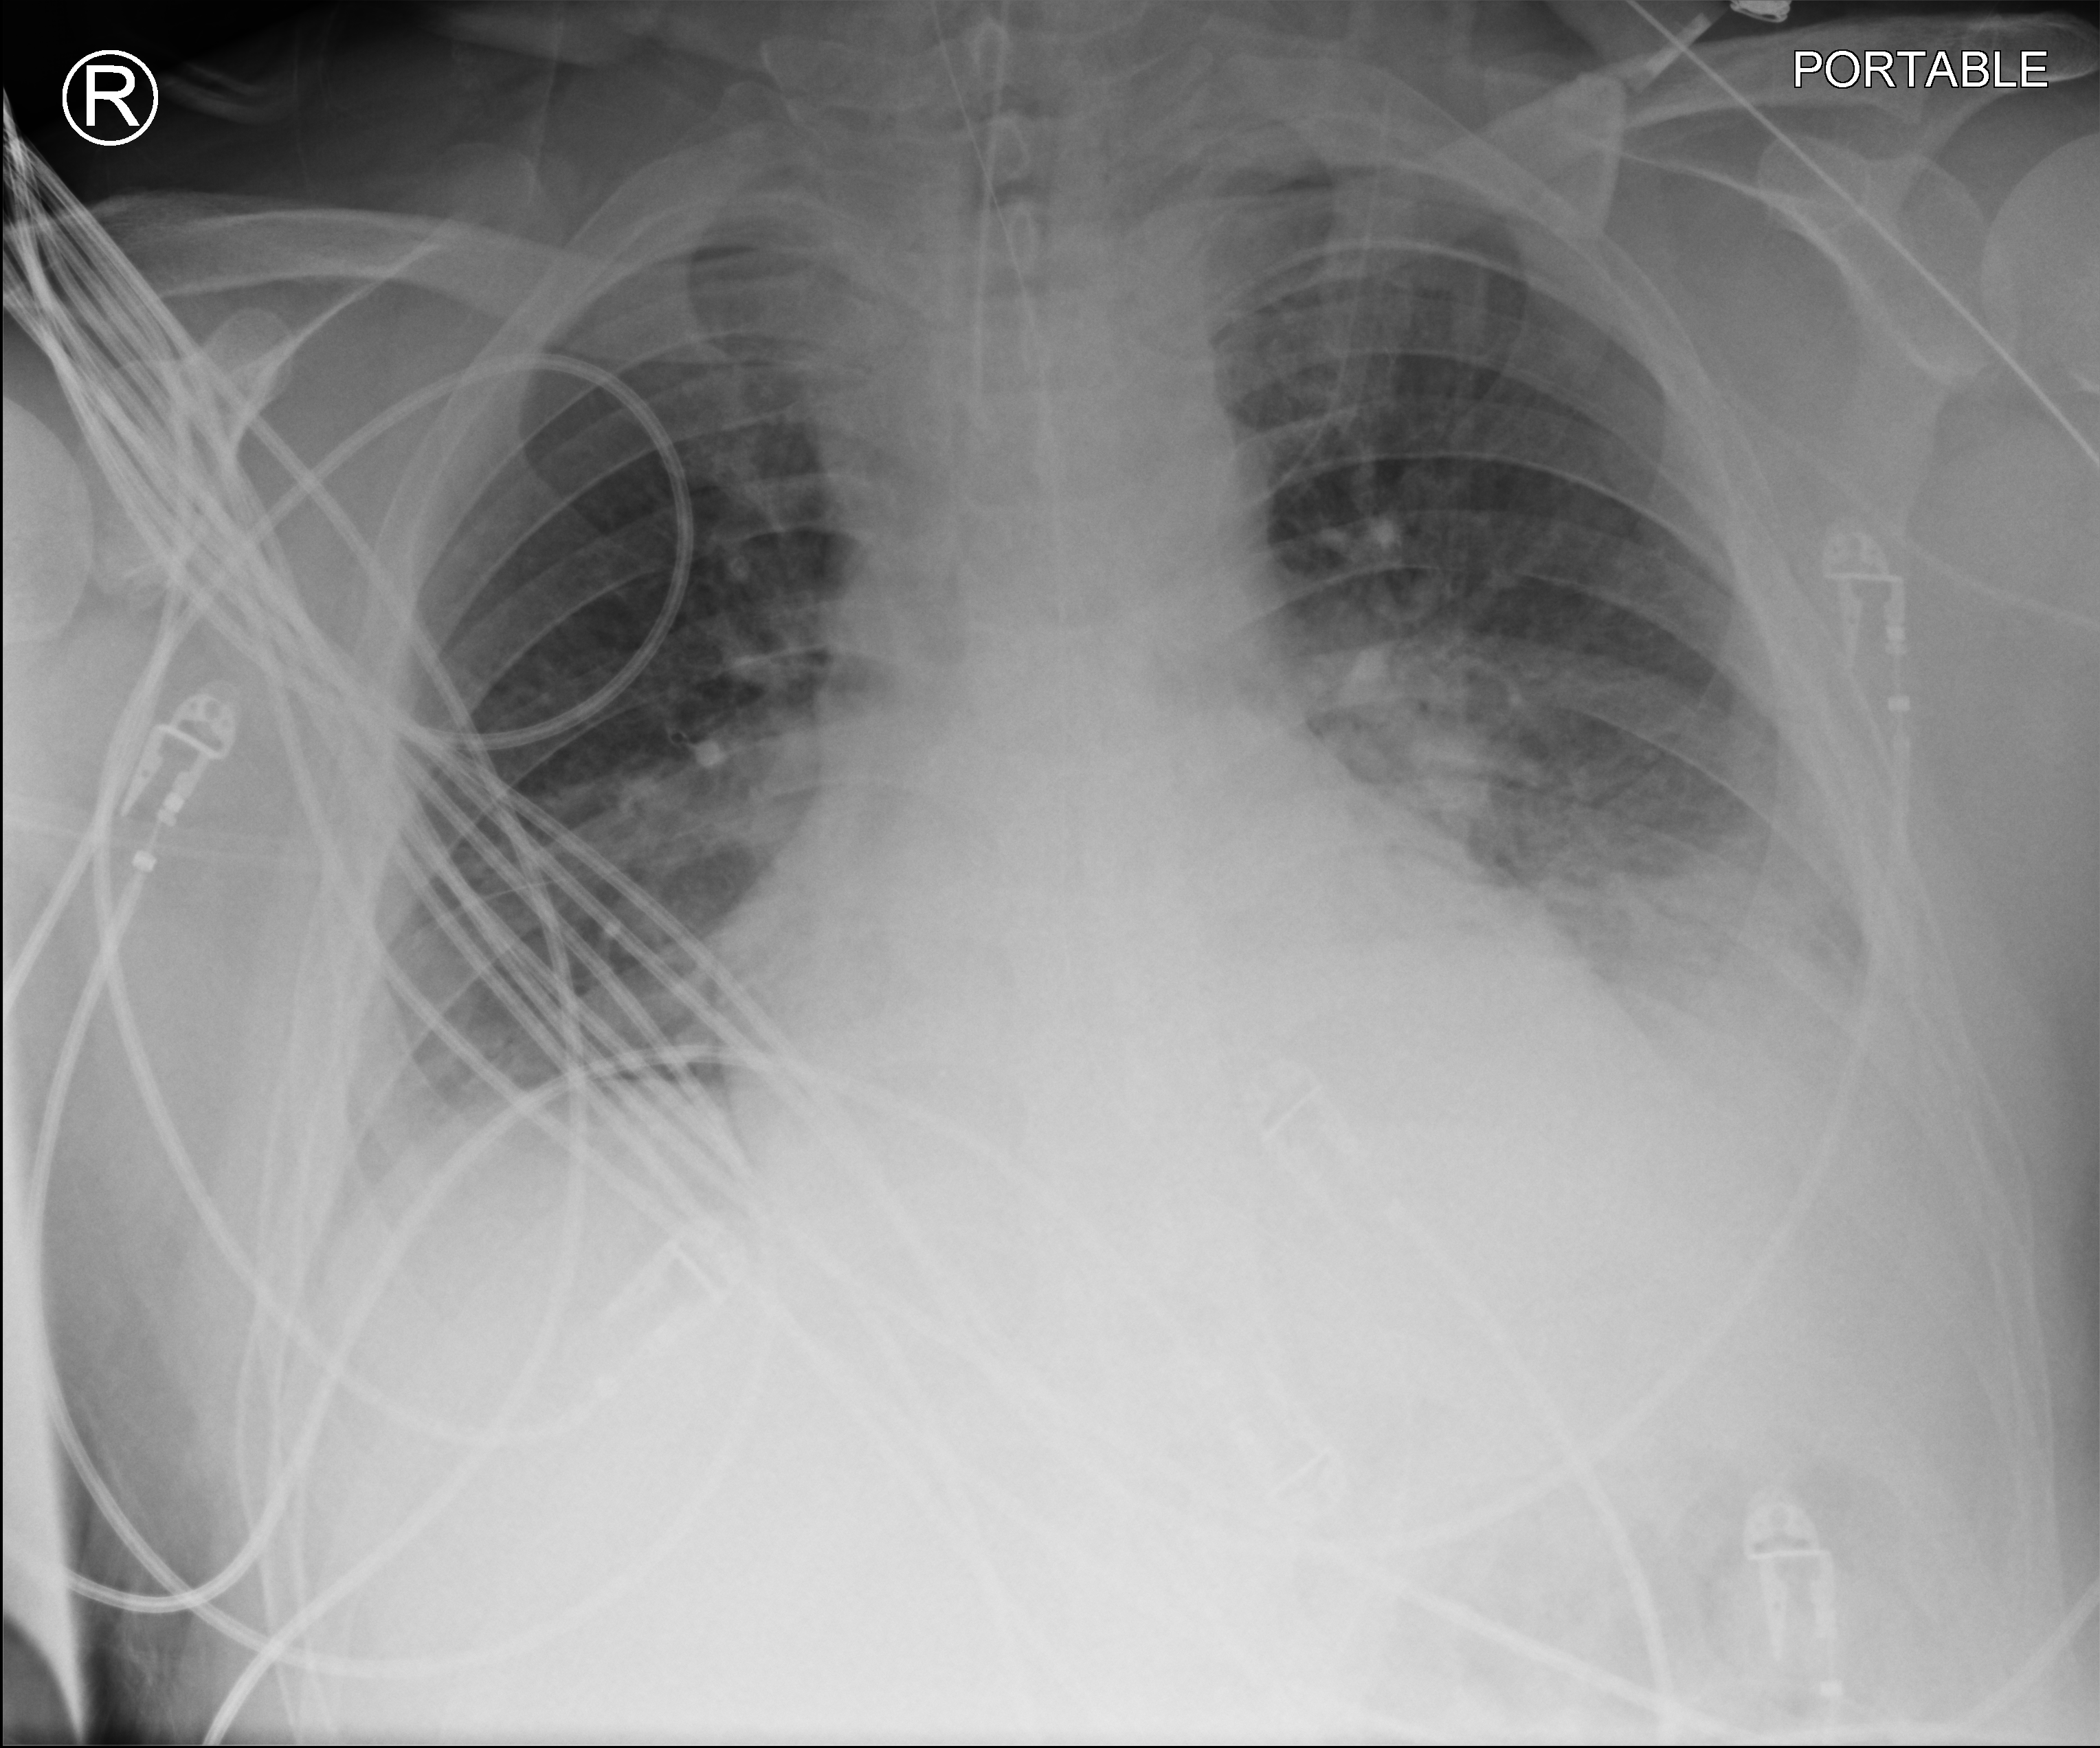
Bedside chest radiograph (computed radiography), anteroposterior (AP) projection. Patient hospitalised with COVID-19; male, aged 18–59 years.
Admission-level facts for this patient (not findings on this image; timing relative to this image not recorded): mechanically ventilated during this hospital stay: yes.